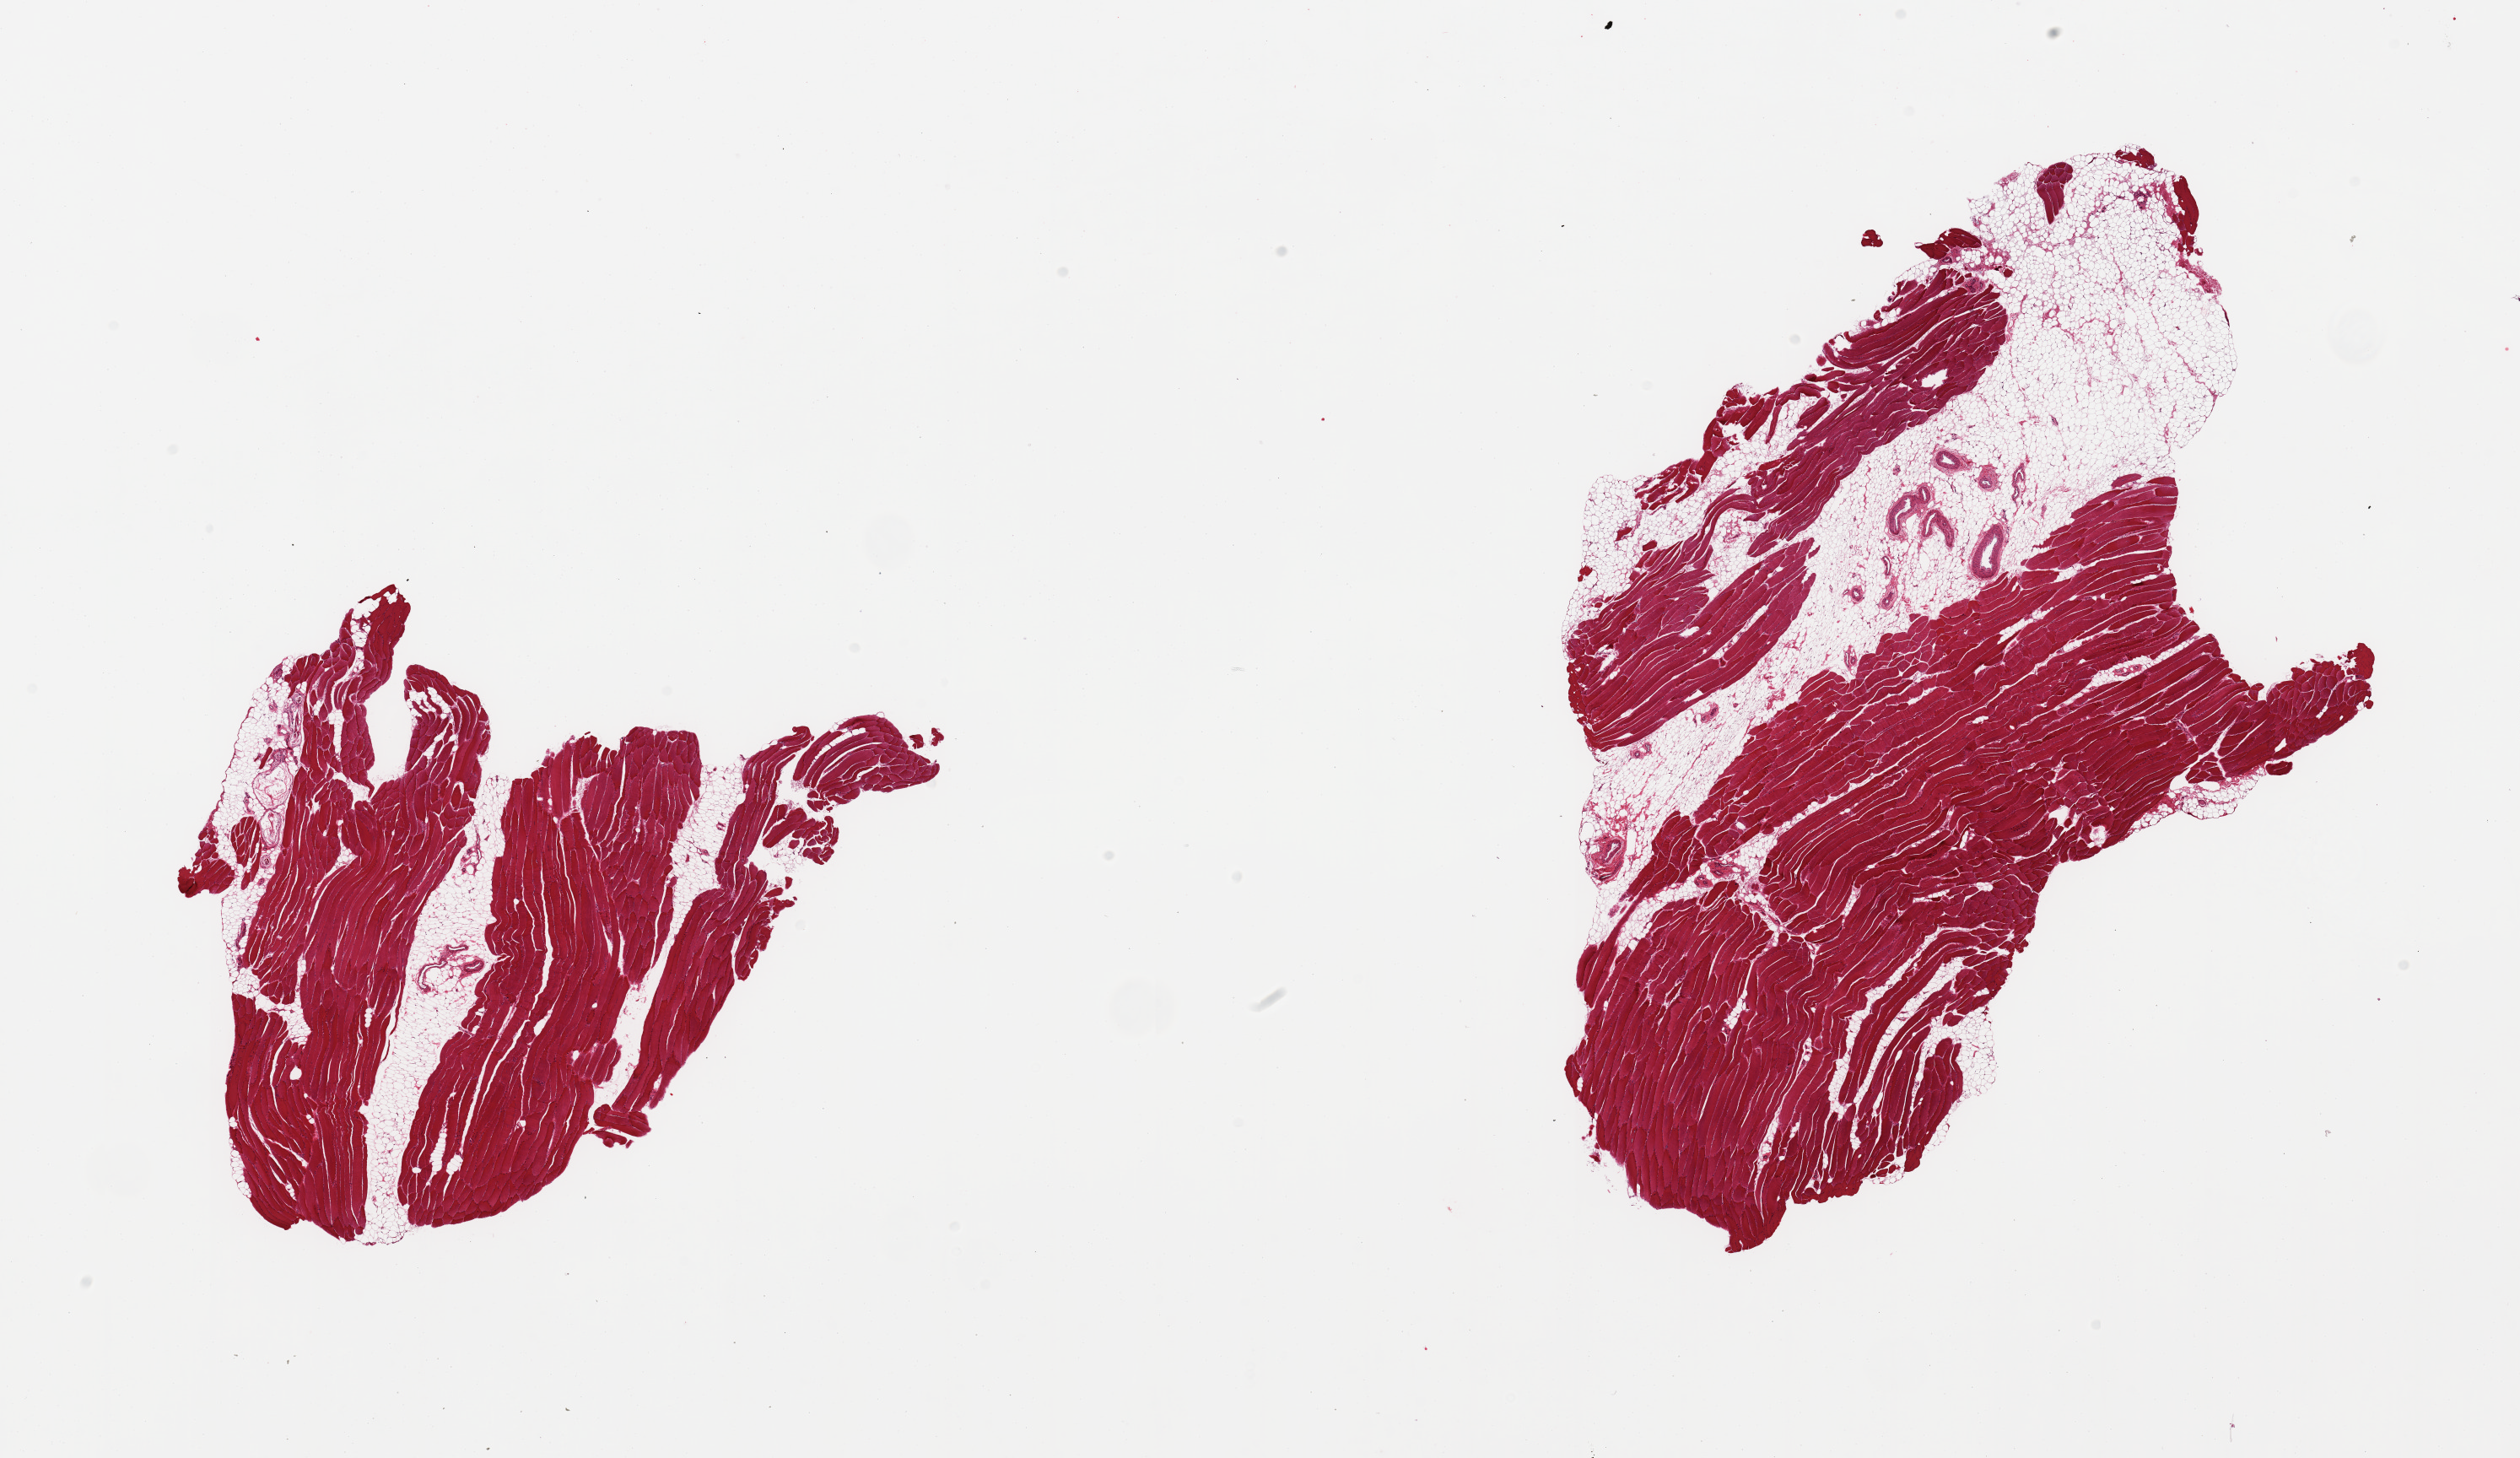
Whole-slide image, hematoxylin and eosin (H&E) stain — shown as a low-resolution overview of the whole scanned area (about 23.6 x 13.7 mm). PAXgene-fixed paraffin-embedded (PFPE) section. Section of skeletal muscle (target tissue). Tissue donor sample. Male donor.
Reviewer comment on this tissue sample: 2 pieces; 10% & 30% internal fat content.